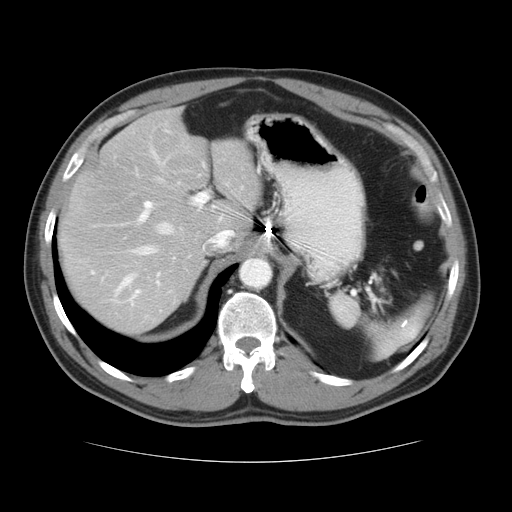
Contrast-enhanced abdominal CT, one axial slice. Position 25 of 37 along the scan axis. 120 kVp. Intravenous contrast given. Soft-tissue window (W 400 / L 40 HU). 5 mm slice thickness. 512 × 512 image matrix, field of view 374 × 374 mm. Male patient, age 66 years. From the clinical record (not read from this slice): diagnosis: colorectal cancer liver metastases, imaged before liver resection; multiple liver metastases: yes; largest metastasis: 1.6 cm; disease in both lobes: yes.
Outlined on this slice (expert manual segmentation):
- hepatic veins: box from (x=115, y=149) to (x=235, y=294) px
- liver: (x=58, y=108)–(x=261, y=335)
- planned liver remnant (the part of the liver to remain after resection): (x=58, y=140)–(x=261, y=335)
- portal vein (with intrahepatic branches): (x=92, y=192)–(x=209, y=300)